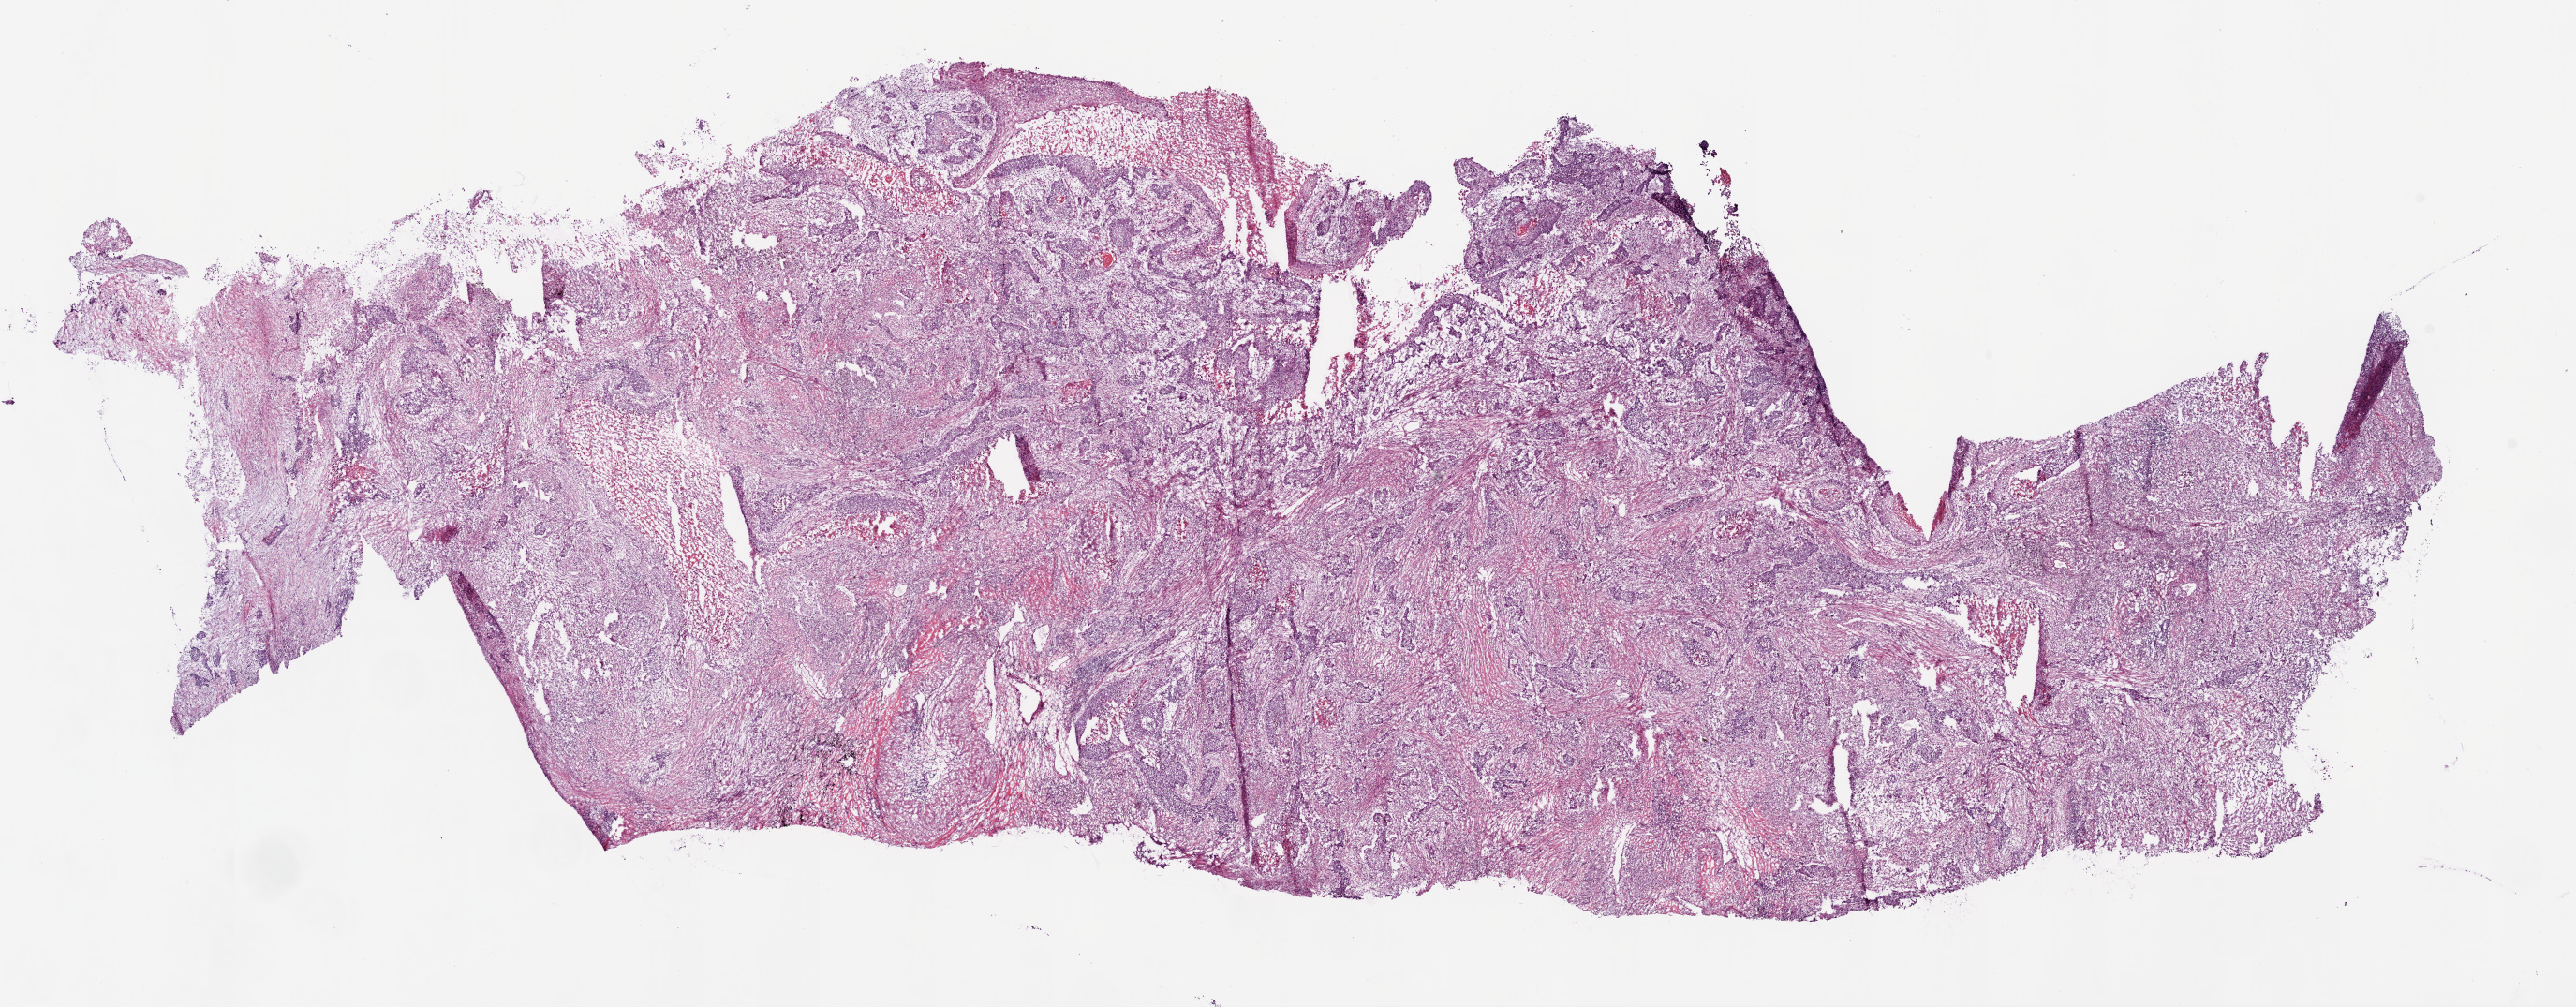
Digitized H&E tissue section (whole slide), low-resolution overview of the scanned area, about 22.1 x 8.6 mm (from a 20x scan). Frozen section. Sample: primary tumour, lung. Male patient; age at initial diagnosis 60 years. Composition of this section per pathologist review: tumour cells 55%, tumour nuclei 70%, normal cells 0%, stromal cells 25%, necrosis 20%.
AJCC pathologic stage: IIB. Diagnosis: Squamous cell carcinoma, NOS (upper lobe, lung). TNM: T3 N0 M0.